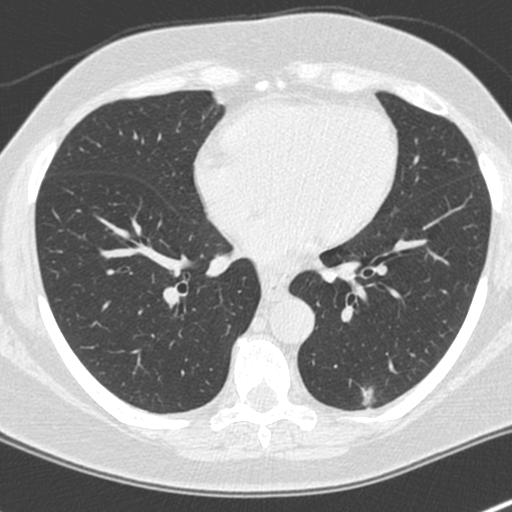
Axial slice from a low-dose chest CT screening exam; baseline screening round; lung window (W 1500 / L -600 HU); 1.3 mm slice thickness; 120 kVp; slice 118 of 222 in the series; 512 × 512 image matrix, field of view 300 × 300 mm. Female participant, aged 64 years at enrolment.
- Expert-annotated lung lesion, bounding box (x1, y1, x2, y2) in pixels: (346, 372, 393, 419).
- No non-calcified nodule or mass ≥4 mm was recorded by the screening reader at this exam.
- Participant outcome: lung cancer diagnosed 549 days after this screen (after the second annual screen) — adenocarcinoma, NOS, left lower lobe, poorly differentiated (G3), stage IA (AJCC 6th edition), 8 mm at pathology.